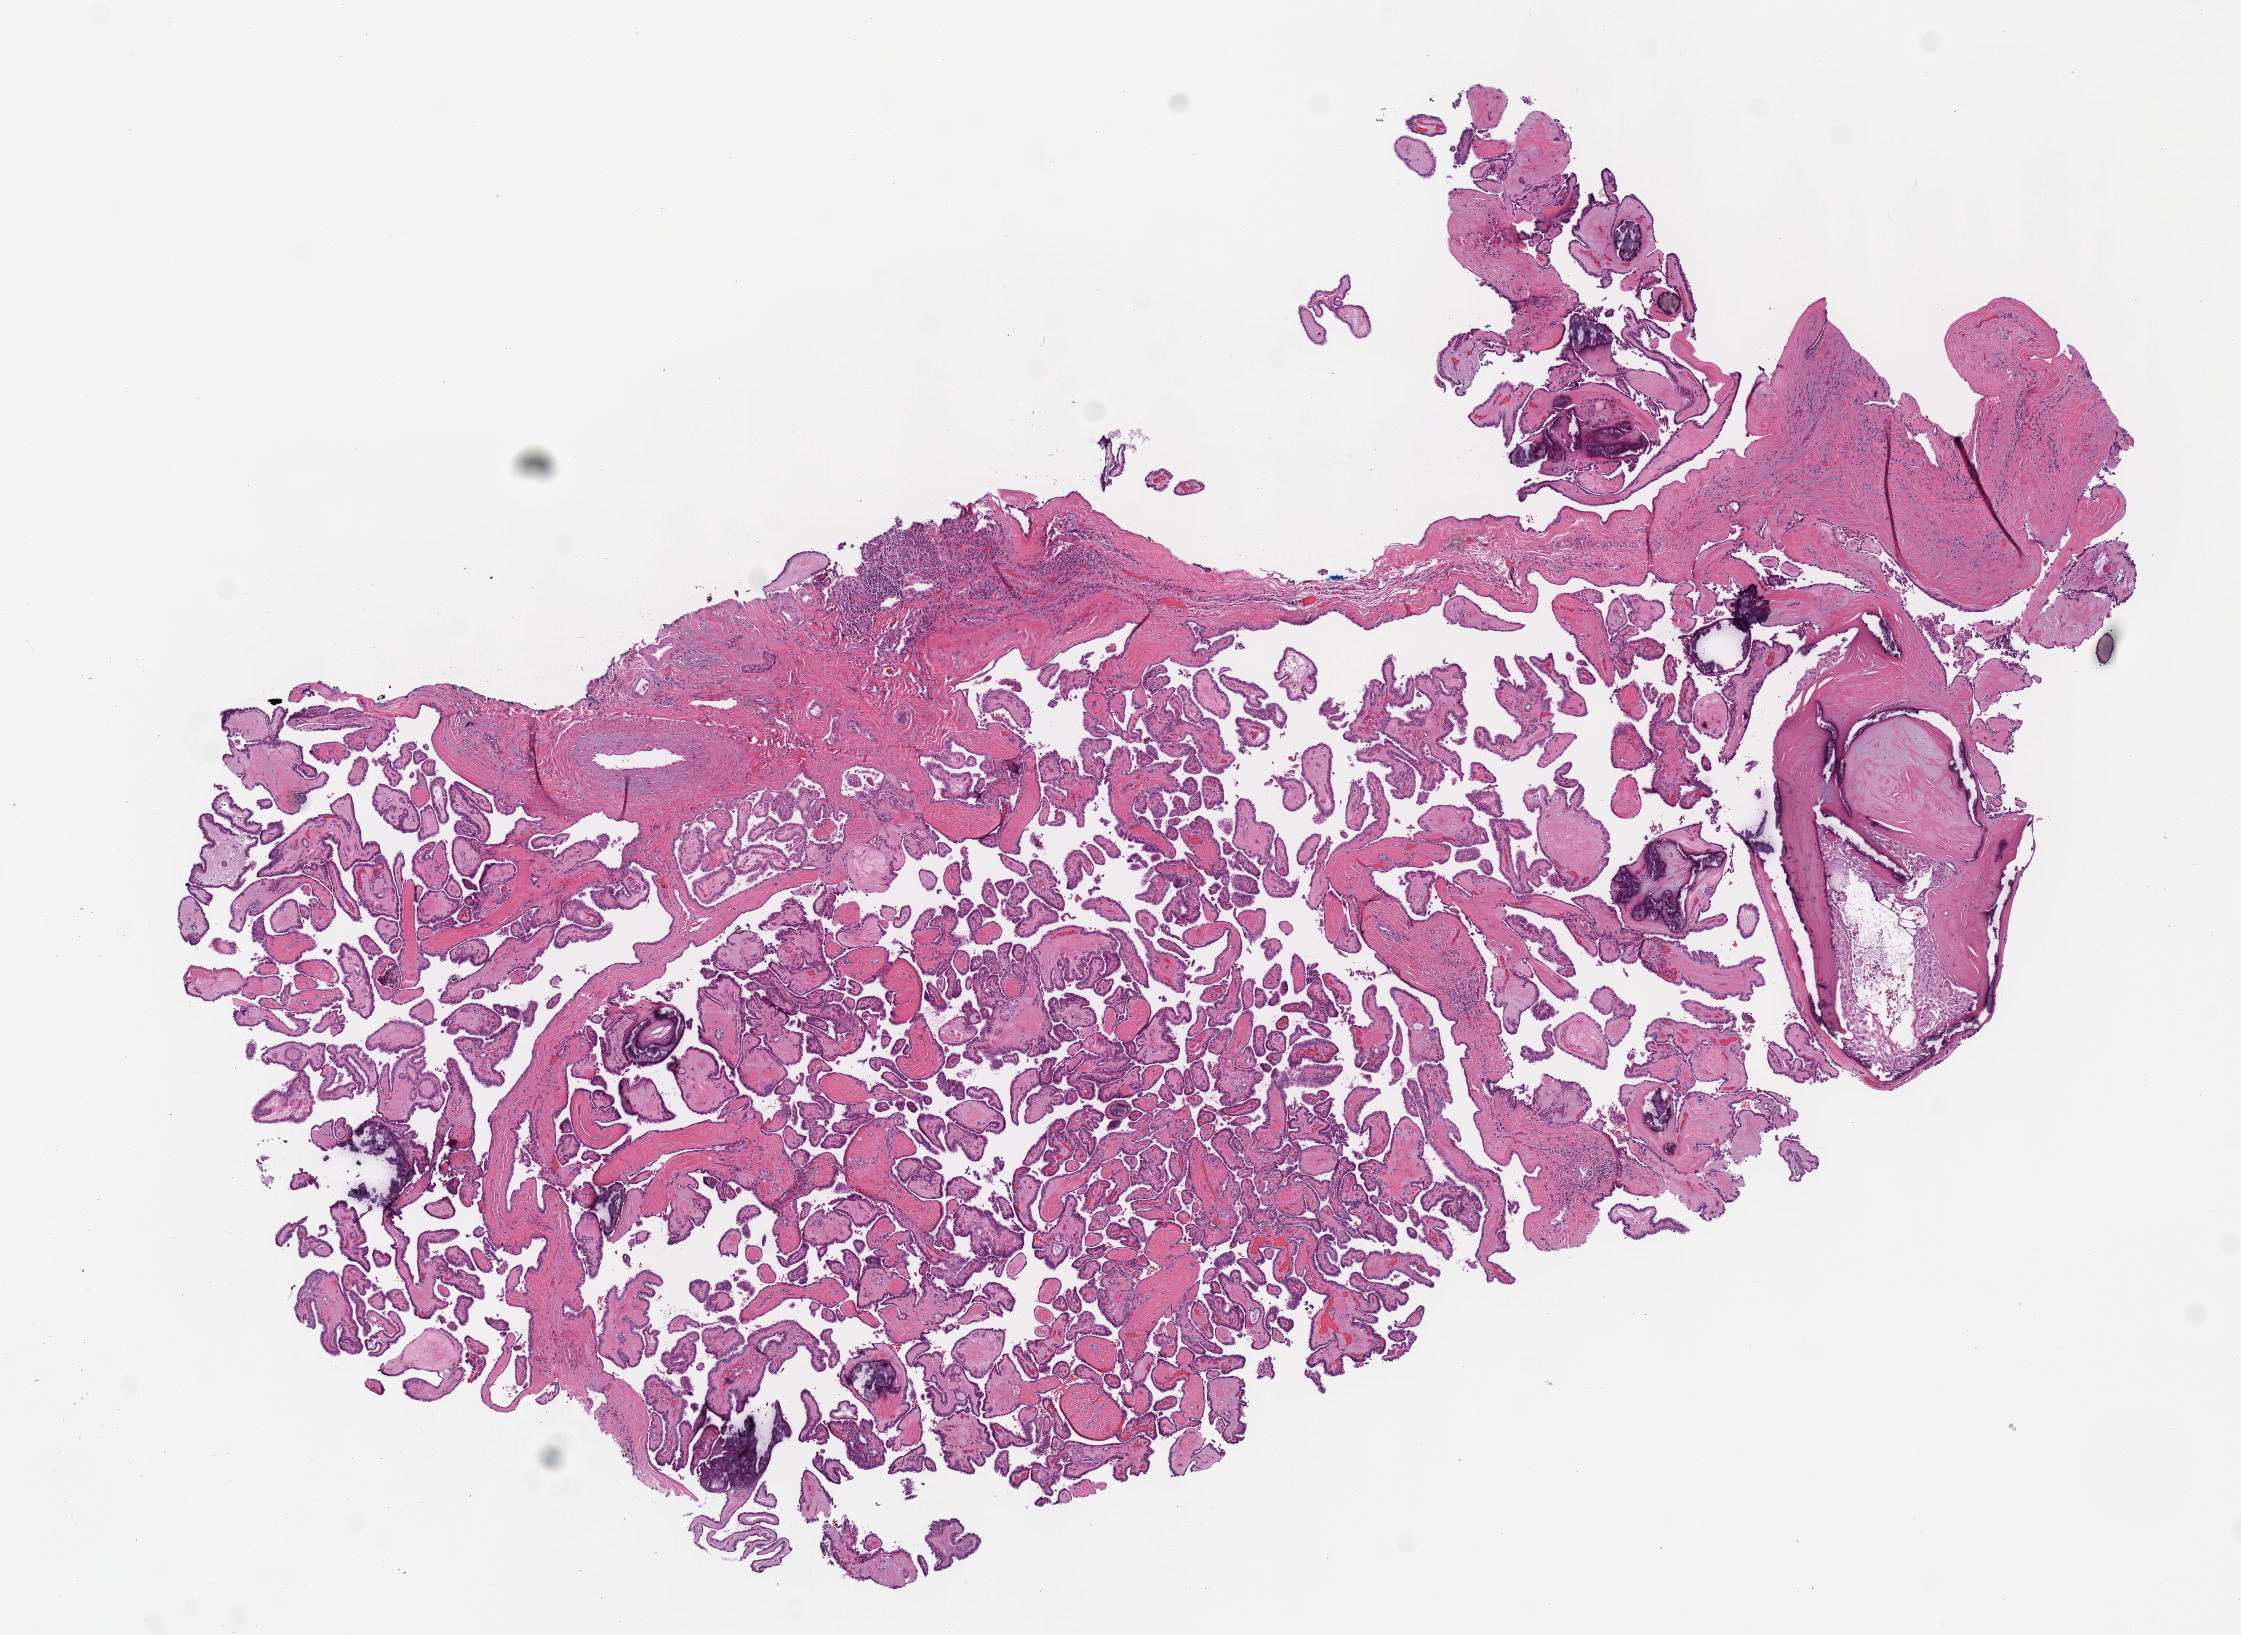
Digitized Hematoxylin and eosin (H&E) stained tissue section (whole slide) — a low-resolution overview of the entire scanned area, about 8.8 x 6.4 mm. FFPE section. Primary tumour sample from the thyroid. Patient: male, age at initial diagnosis 20 years.
Pathologic diagnosis: Papillary adenocarcinoma, NOS.